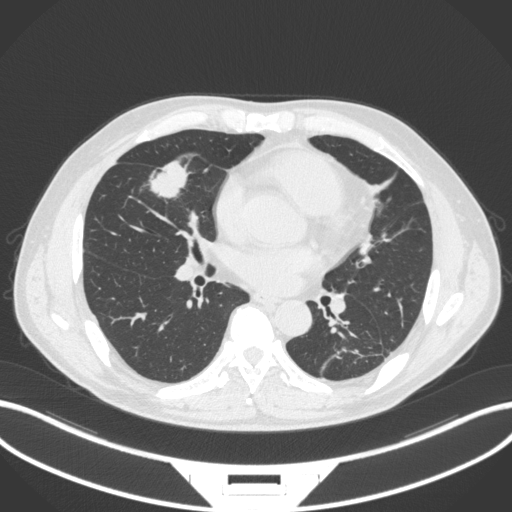
Chest CT, one axial slice. Slice 142 of 399 in the series (ordered by position). Reconstruction kernel B31f. Lung window (W 1500 / L -600 HU). 512 × 512 image matrix. Patient: male, 59 years. From the clinical record (not read from this slice): clinical TNM (as recorded): T2a N1 M0.
Structures marked on this image (bounding box drawn by a radiologist):
- lung tumour (recorded histology: adenocarcinoma): bounding box <144,157,193,200> (left, top, right, bottom; pixels)